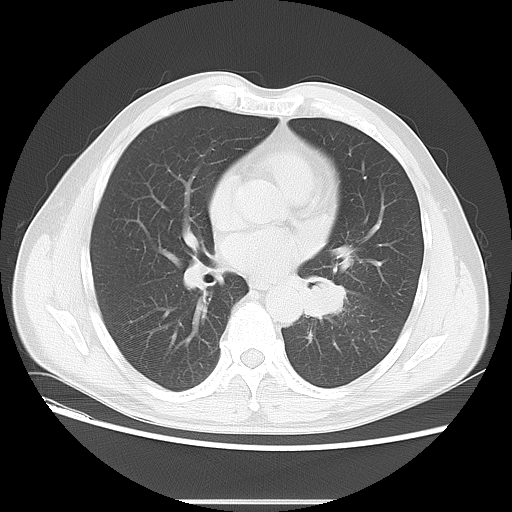
Chest CT, one axial slice. Position 28 of 59 along the scan axis. Reconstruction kernel LUNG. Lung window (W 1500 / L -600 HU). 512 × 512 image matrix. Male patient, age 59 years. Case-level facts recorded for this patient, not image findings: clinical TNM (as recorded): T2 N3 M0.
Annotated regions visible in this slice (rectangle marked by the reading radiologist):
- lung tumour (recorded histology: small cell carcinoma): box from (x=304, y=277) to (x=354, y=319) px